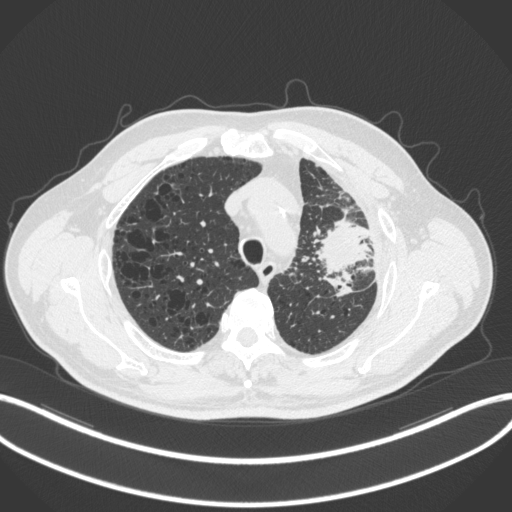
Chest CT, one axial slice; position 239 of 286 along the scan axis; reconstruction kernel B31f; 120 kVp; lung window (W 1500 / L -600 HU); 1 mm slice thickness; 512 × 512 image matrix. Patient: male, 68 years. From the clinical record (not read from this slice): clinical TNM (as recorded): T3 N3 M1.
Annotated regions visible in this slice (bounding box drawn by a radiologist):
- lung tumour (recorded histology: adenocarcinoma): bounding box (x1, y1, x2, y2) in pixels: (316, 217, 370, 274)